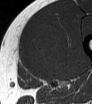
MRI of an extremity soft-tissue mass, one axial slice. Slice 30 of 62 in the series (ordered by position). MR volume resampled by the dataset authors to the PET/CT grid (not the native acquisition matrix). 3.27 mm slice thickness. 92 × 104 image matrix, field of view 90 × 102 mm. Male patient. Case-level facts recorded for this patient, not image findings: histological type: mixoid liposarcoma; grade: low; site of the primary tumour: left thigh.
Annotated regions visible in this slice (expert contour drawn on MRI and transferred to this co-registered scan by the dataset authors):
- gross tumour volume (mass): bounding box <21,22,70,80> (left, top, right, bottom; pixels)